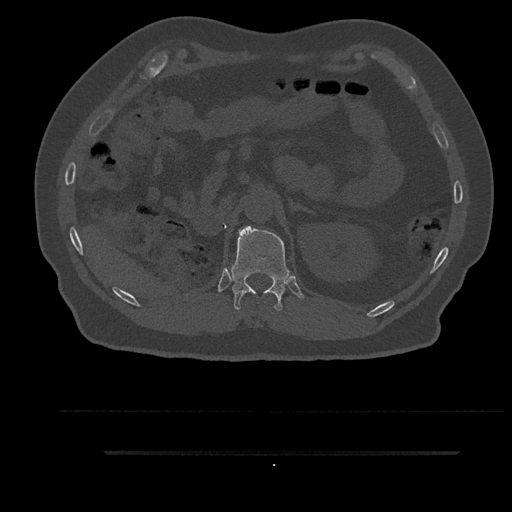
CT including the spine, one axial slice; slice 248 of 797 in the series (ordered by position); reconstruction kernel Br40s/3; 120 kVp; bone window (W 1800 / L 400 HU); 0.5 mm slice thickness; 512 × 512 image matrix, field of view 432 × 432 mm. Patient: male, 63 years. From the clinical record (not read from this slice): primary cancer: renal; vertebrae with lytic lesions (as recorded): T8.
Annotated regions visible in this slice (semi-automatic segmentation, software-assisted and operator-edited):
- T12 vertebra: bounding box [x1, y1, x2, y2] px = [229, 226, 292, 311]